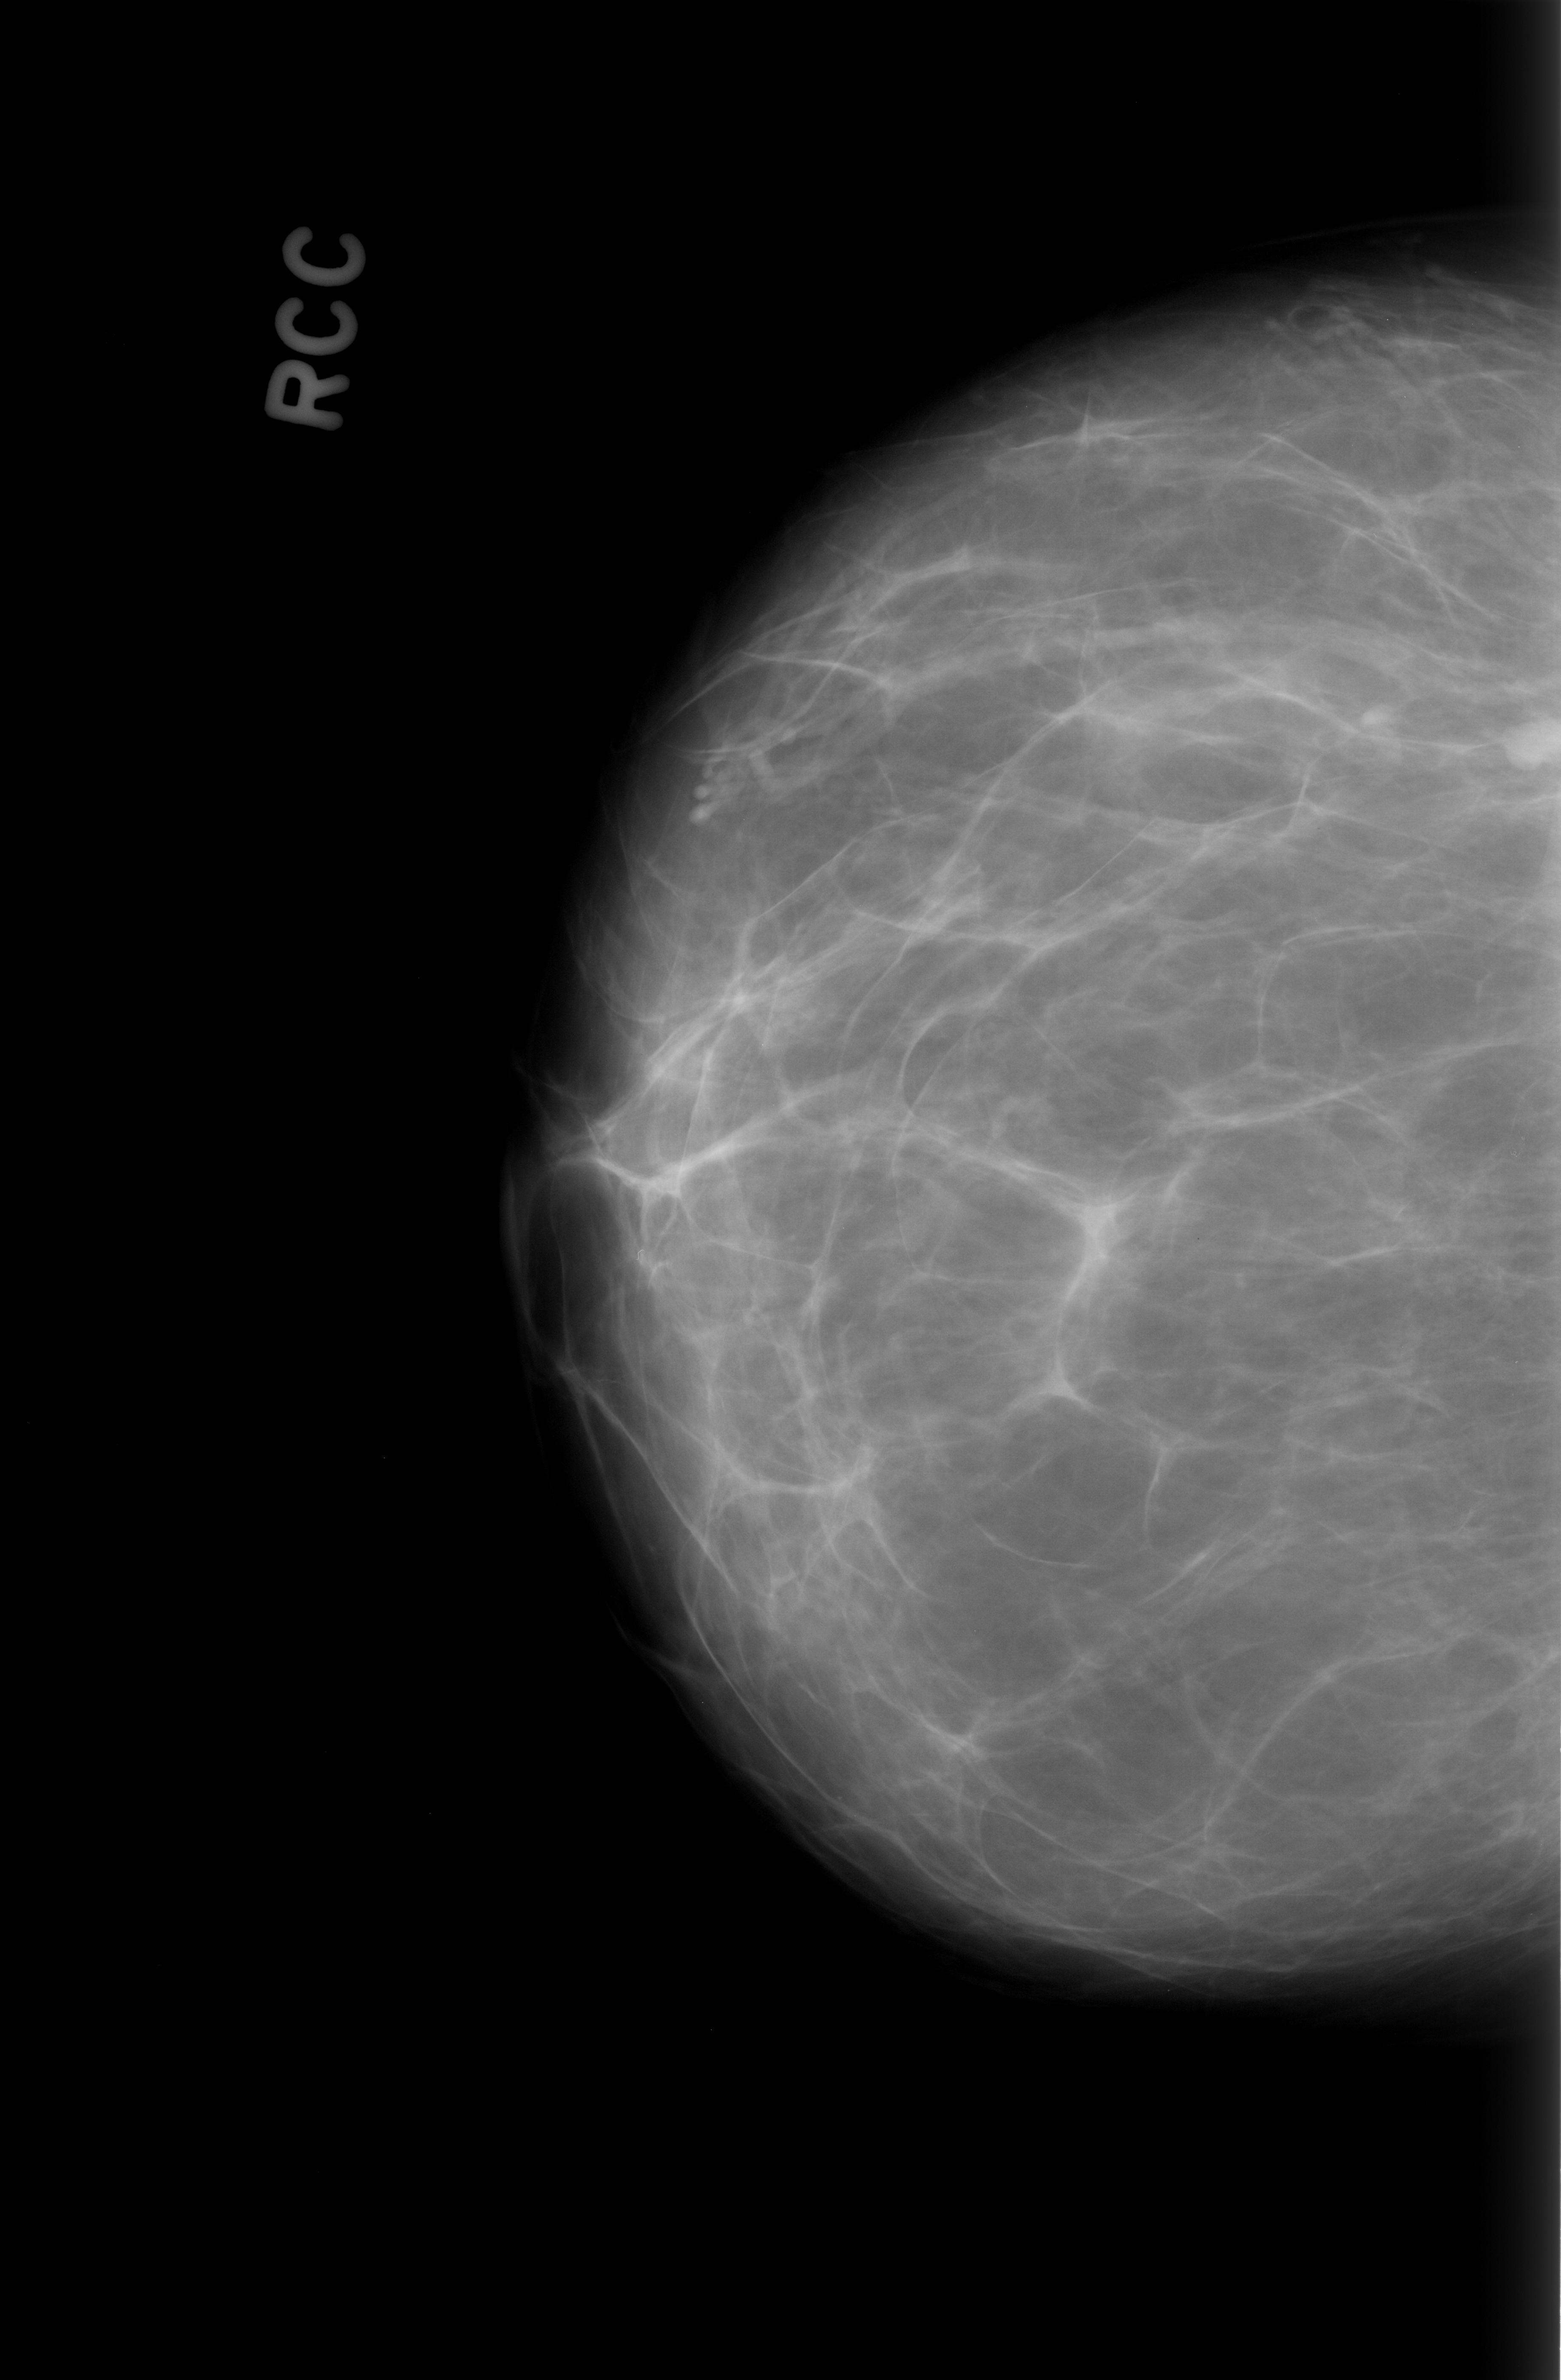
Scanned film-screen mammogram; right breast; craniocaudal (CC) view; breast composition: almost entirely fatty (BI-RADS density category 1 of 4); 1561 × 2380 image matrix.
Marked abnormalities (boxes around the expert regions of interest):
- mass, shape lobulated, margins circumscribed; BI-RADS assessment category 3; subtlety rating 5 on a 1 (subtle) to 5 (obvious) scale; outcome (as recorded, no biopsy): benign without callback (not worked up further): bounding box <1501,708,1561,771> (left, top, right, bottom; pixels)